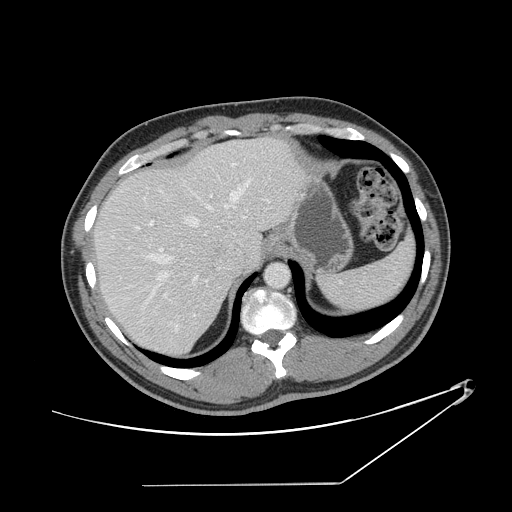
Contrast-enhanced abdominal CT, one axial slice; slice 113 of 152 in the series (ordered by position); reconstruction kernel STANDARD; 120 kVp; soft-tissue window (W 400 / L 40 HU); 2.5 mm slice thickness; 512 × 512 image matrix, field of view 432 × 432 mm. Male patient, age 45 years. From the clinical record (not read from this slice): diagnosis: colorectal cancer liver metastases, imaged before liver resection.
Annotated regions visible in this slice (outlined manually by an expert reader):
- hepatic veins: bounding box (x1, y1, x2, y2) in pixels: (111, 175, 252, 296)
- liver: (96, 138, 303, 356)
- planned liver remnant (the part of the liver to remain after resection): (96, 160, 234, 357)
- portal vein (with intrahepatic branches): (159, 195, 212, 317)